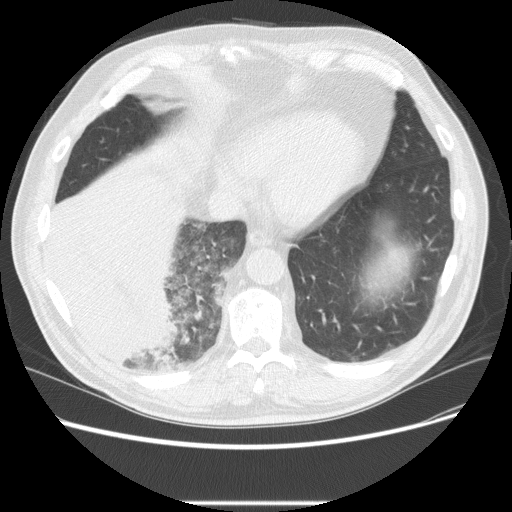
Low-dose screening chest CT, one axial slice. Slice 61 of 233 in the series (ordered by position). Lung window (W 1500 / L -600 HU). 2.5 mm slice thickness. 512 × 512 image matrix, field of view 380 × 380 mm.
Outlined on this slice (expert manual segmentation):
- lesion 3 (tumor, lower lobe of right lung): box from (x=48, y=197) to (x=182, y=370) px